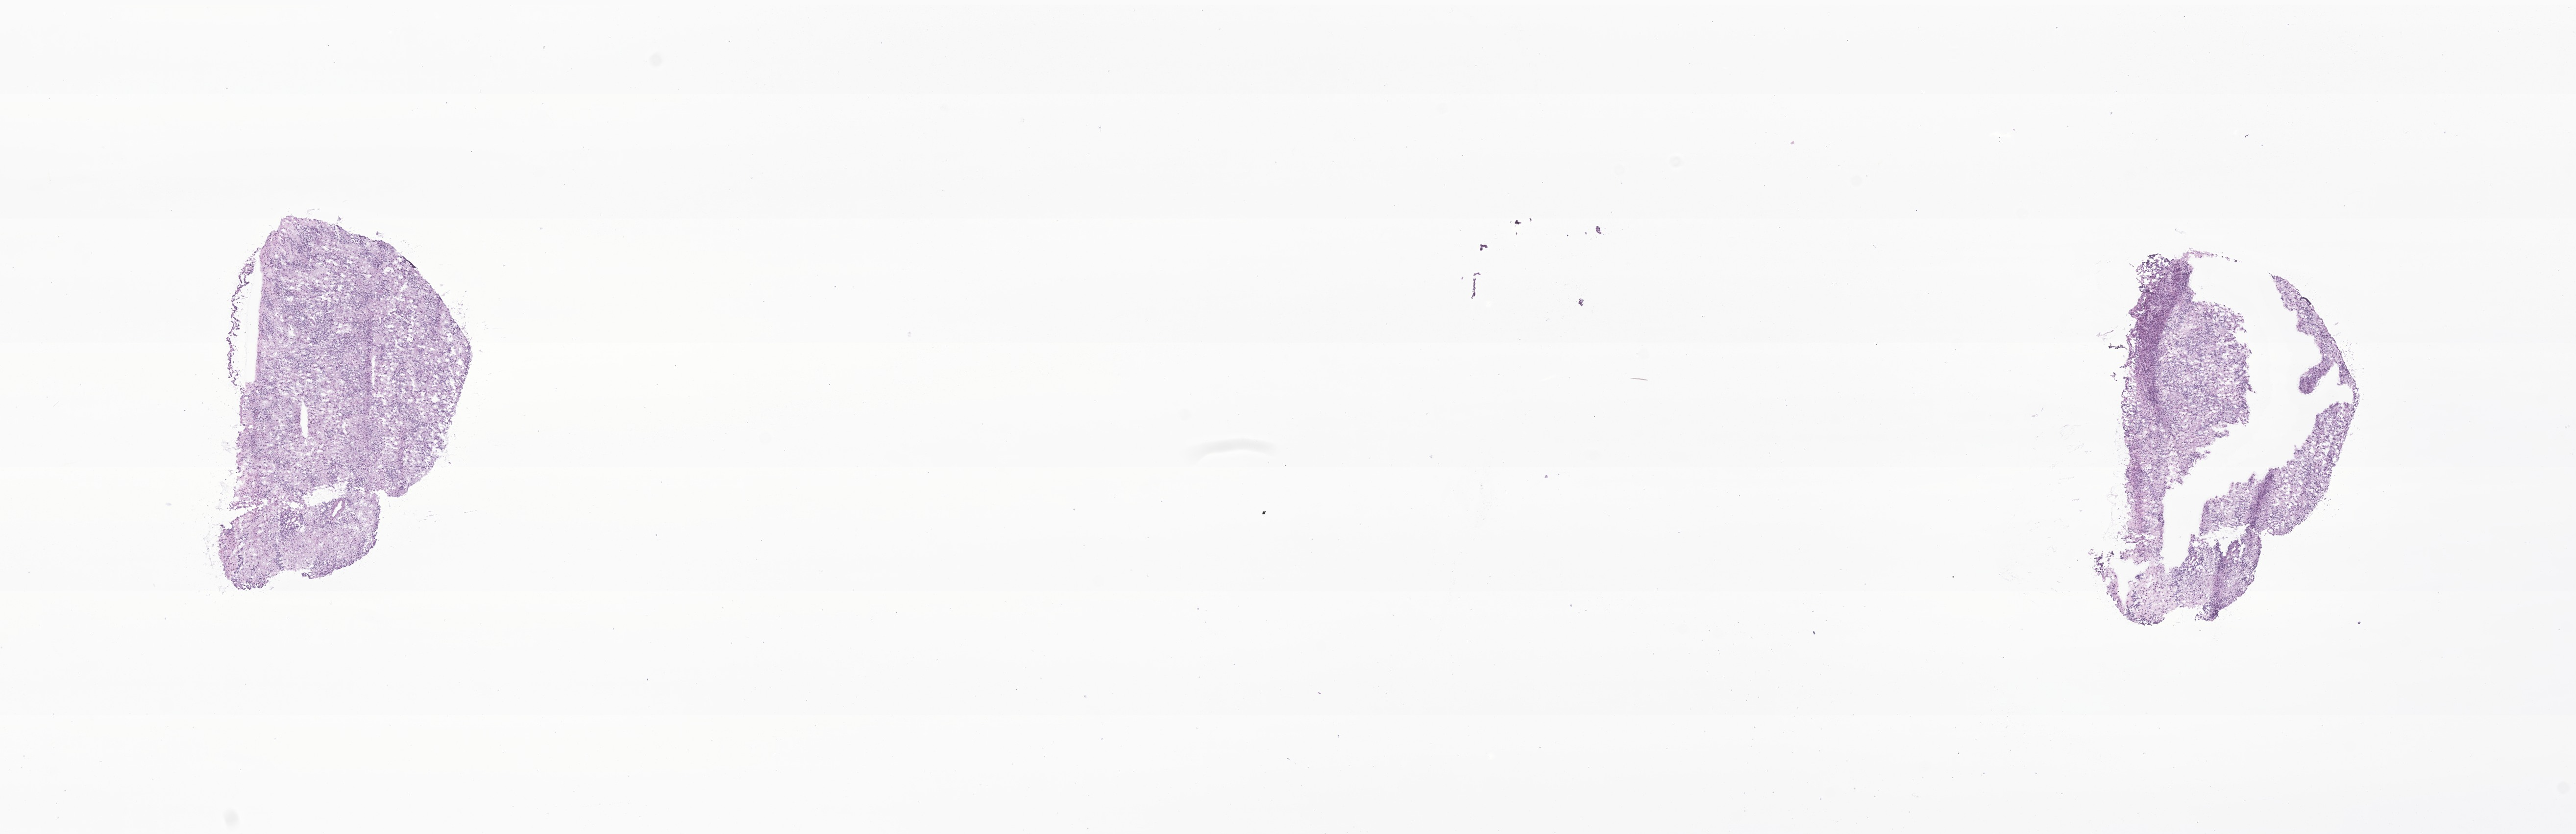
Digitized haematoxylin and eosin-stained section of tumor tissue from the parietal lobe, low-resolution overview of the scanned area, about 22.2 x 7.2 mm; frozen section (OCT-embedded). Female patient, age 940 days (about 2.6 years).
Recorded diagnosis: Embryonal carcinoma, NOS.